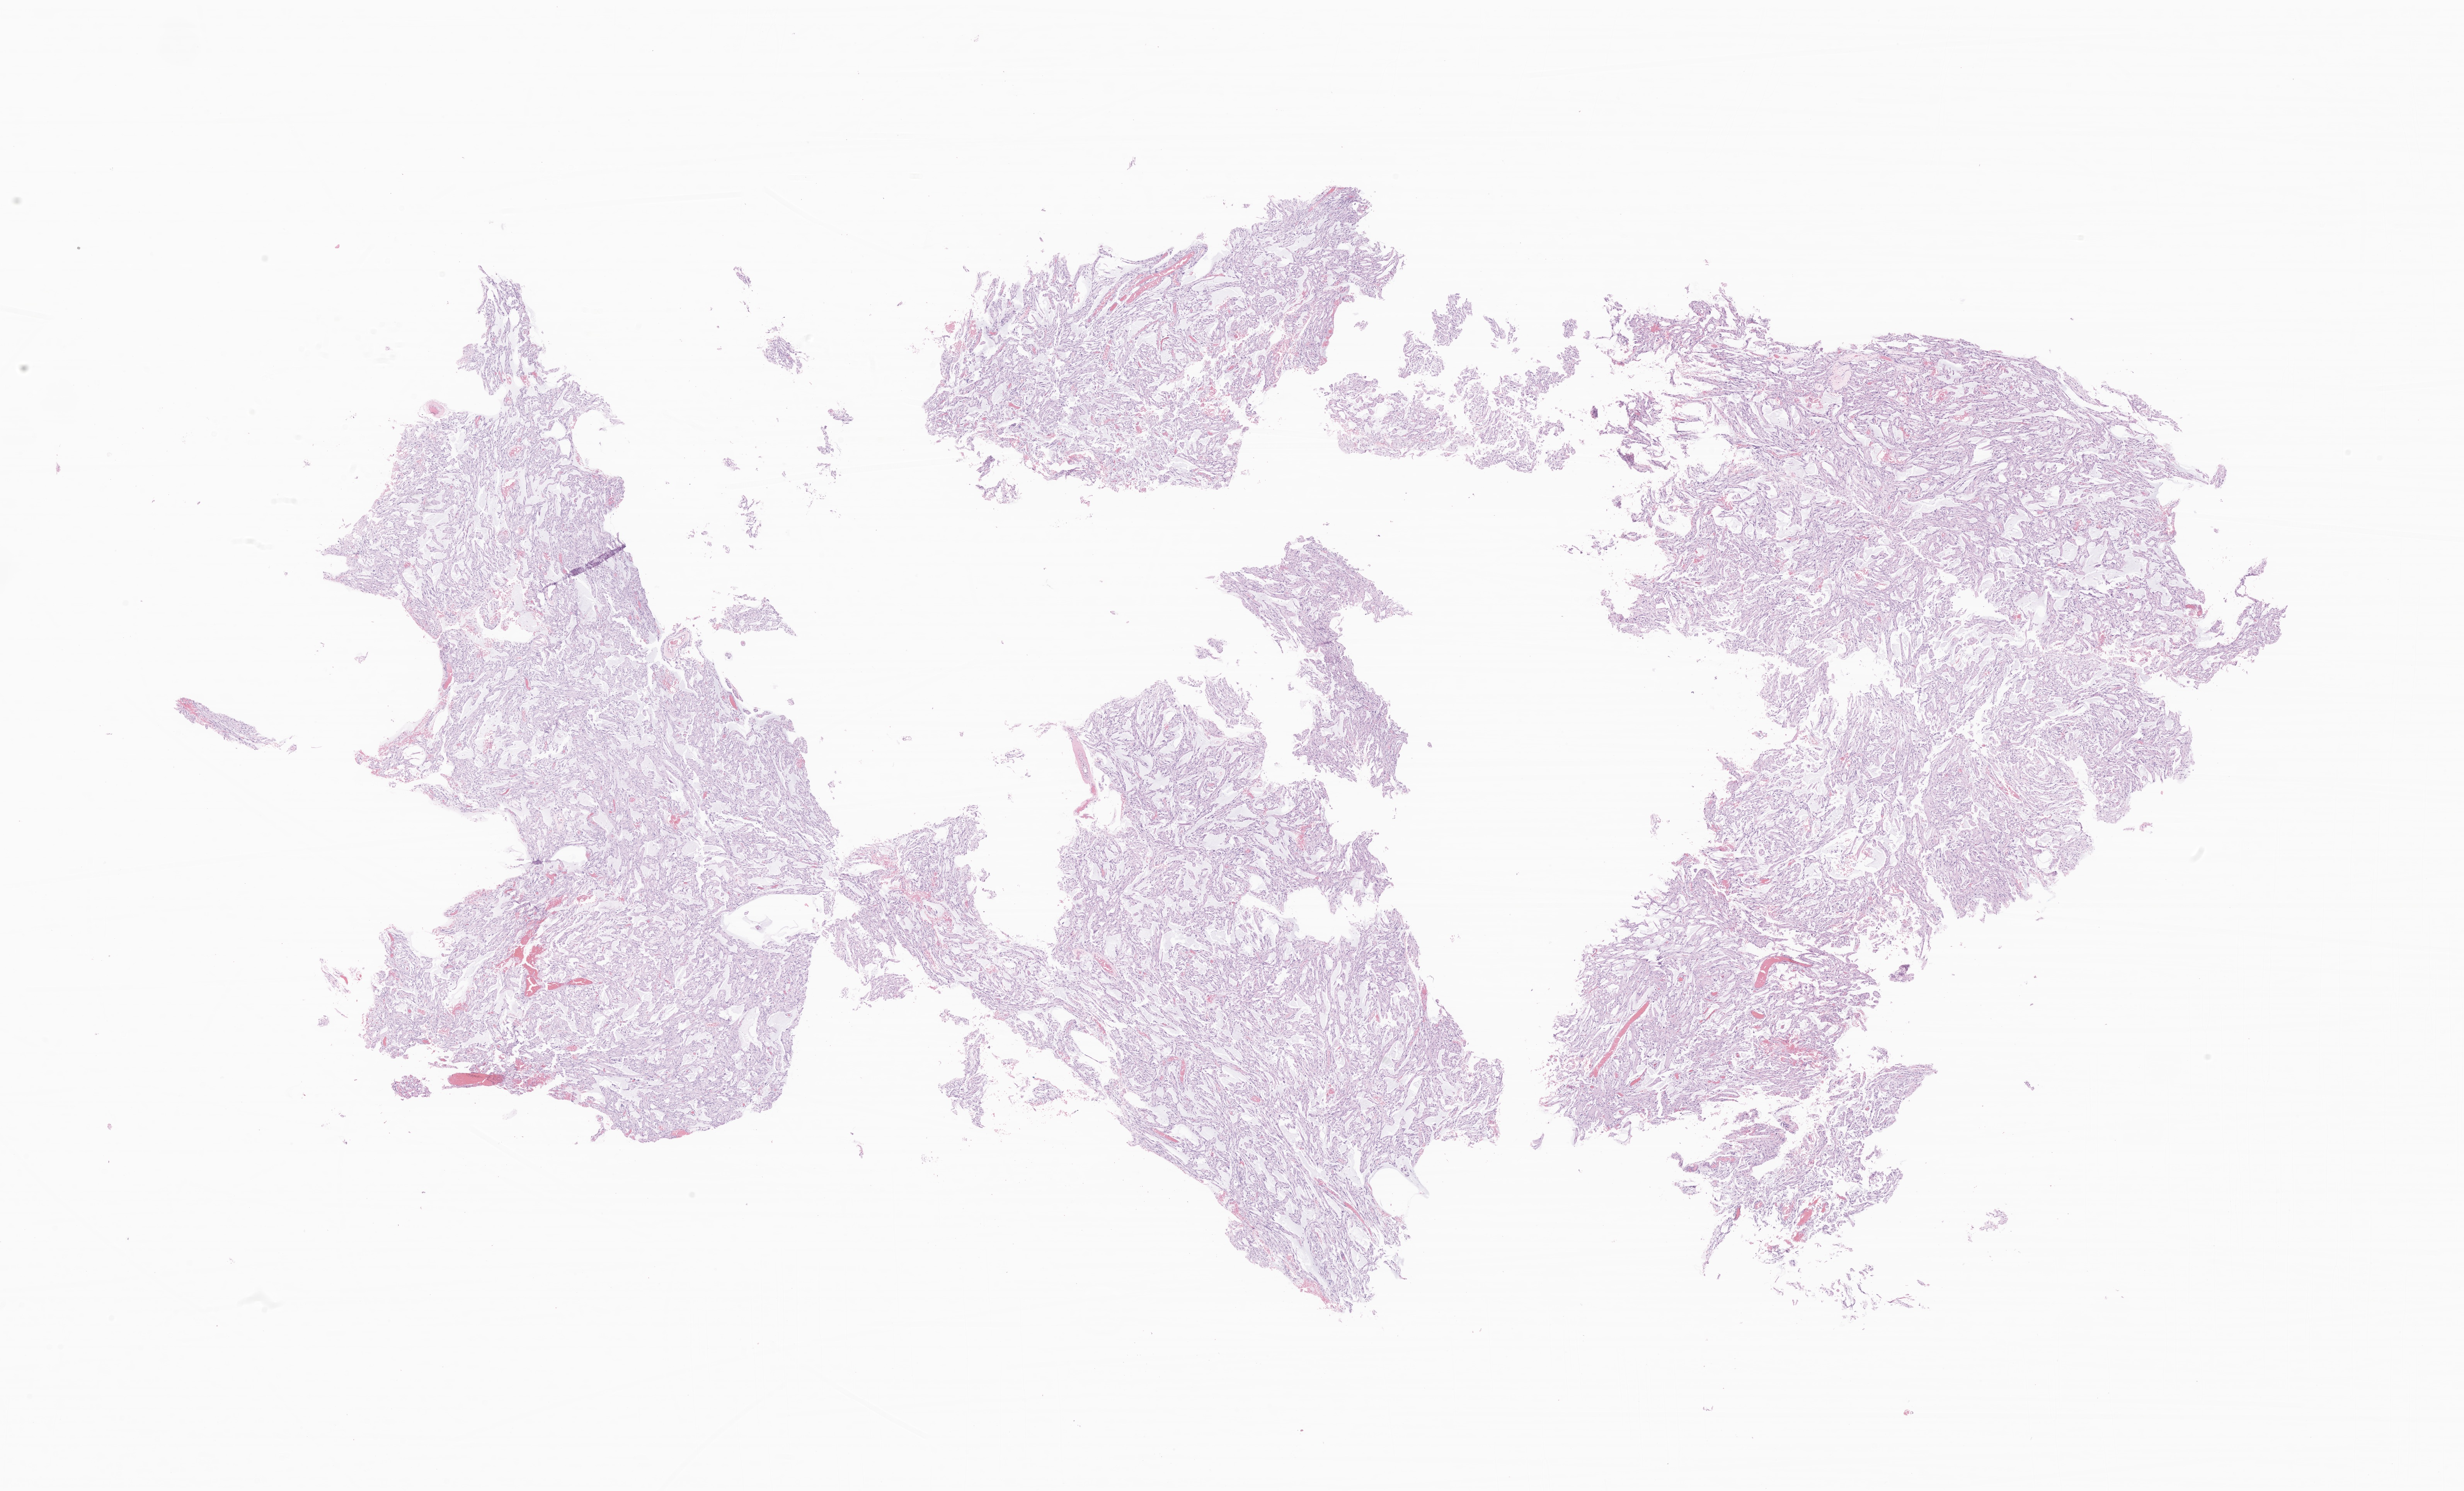
Whole-slide image, hematoxylin and eosin (H&E) stain of tumor tissue from the frontal lobe — whole scanned area (about 26.9 x 16.3 mm) shown as a low-resolution overview, formalin-fixed paraffin-embedded section. Patient male; age 204 months (17 years).
Recorded diagnosis: Pilocytic astrocytoma.